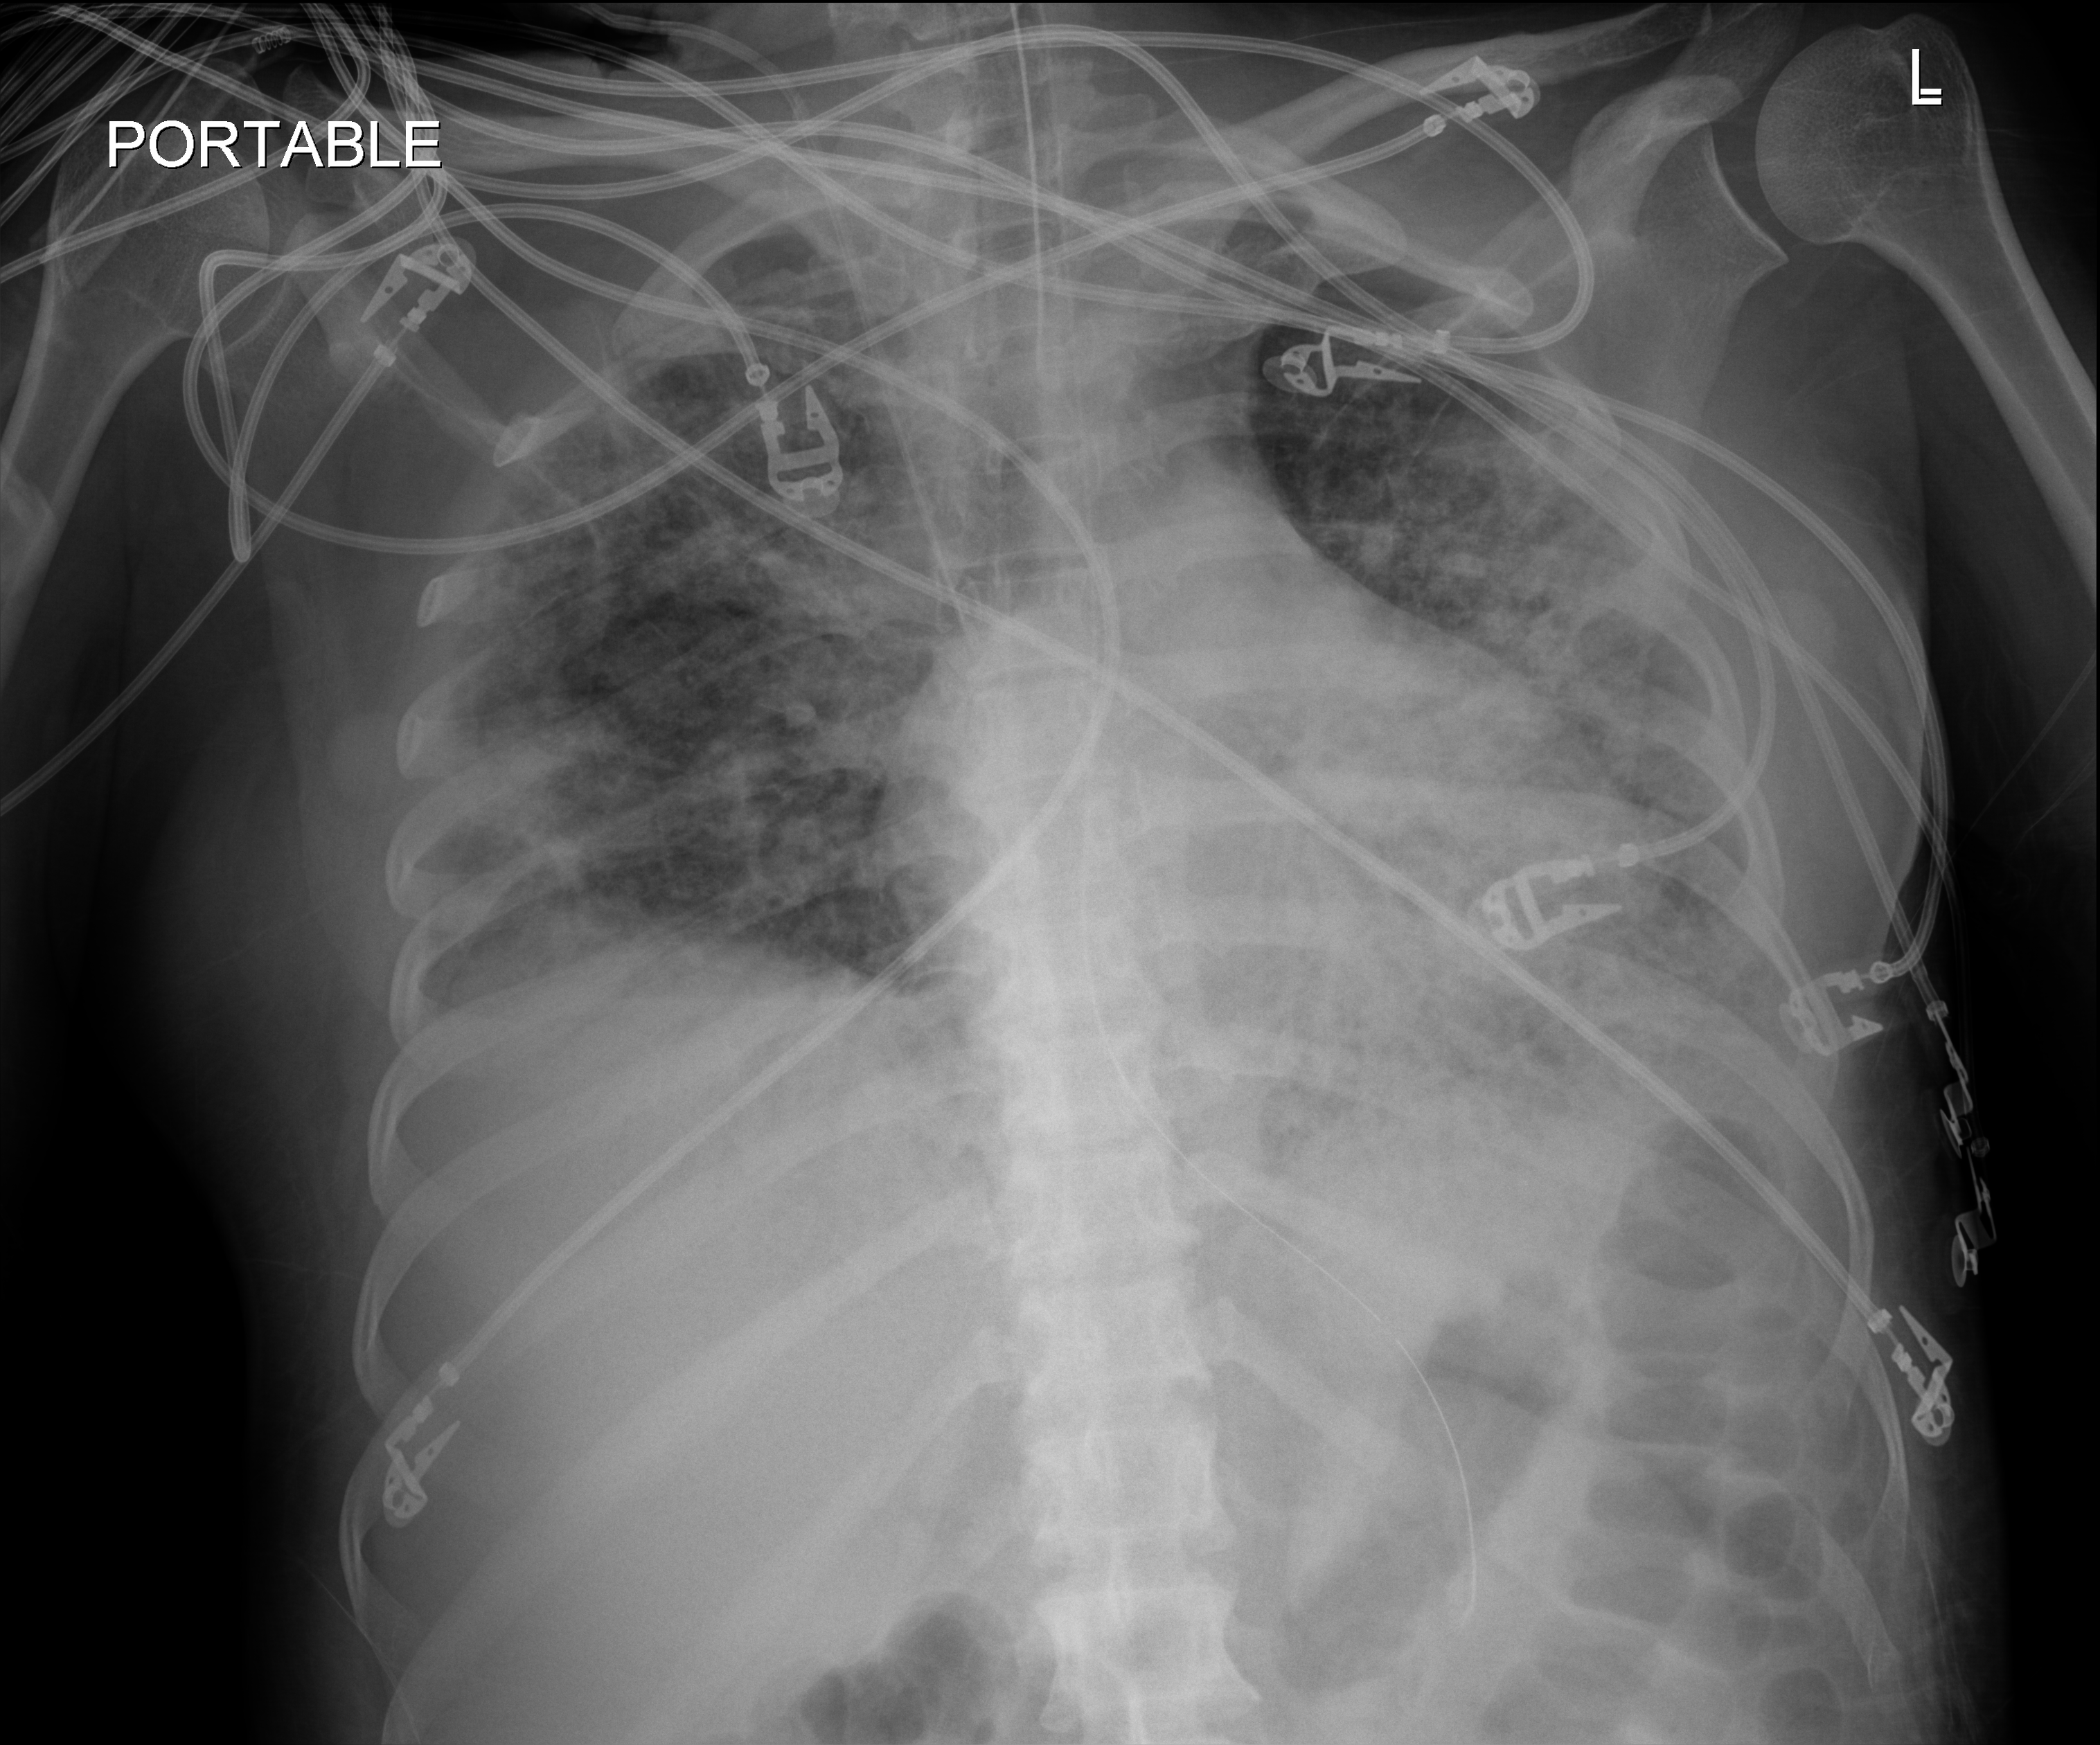
Portable chest radiograph; anteroposterior (AP) projection. Female patient hospitalised with COVID-19, age 18–59 years.
Hospital-stay facts (about this admission, not read from this image; timing relative to this image not recorded):
- mechanically ventilated during this hospital stay: yes